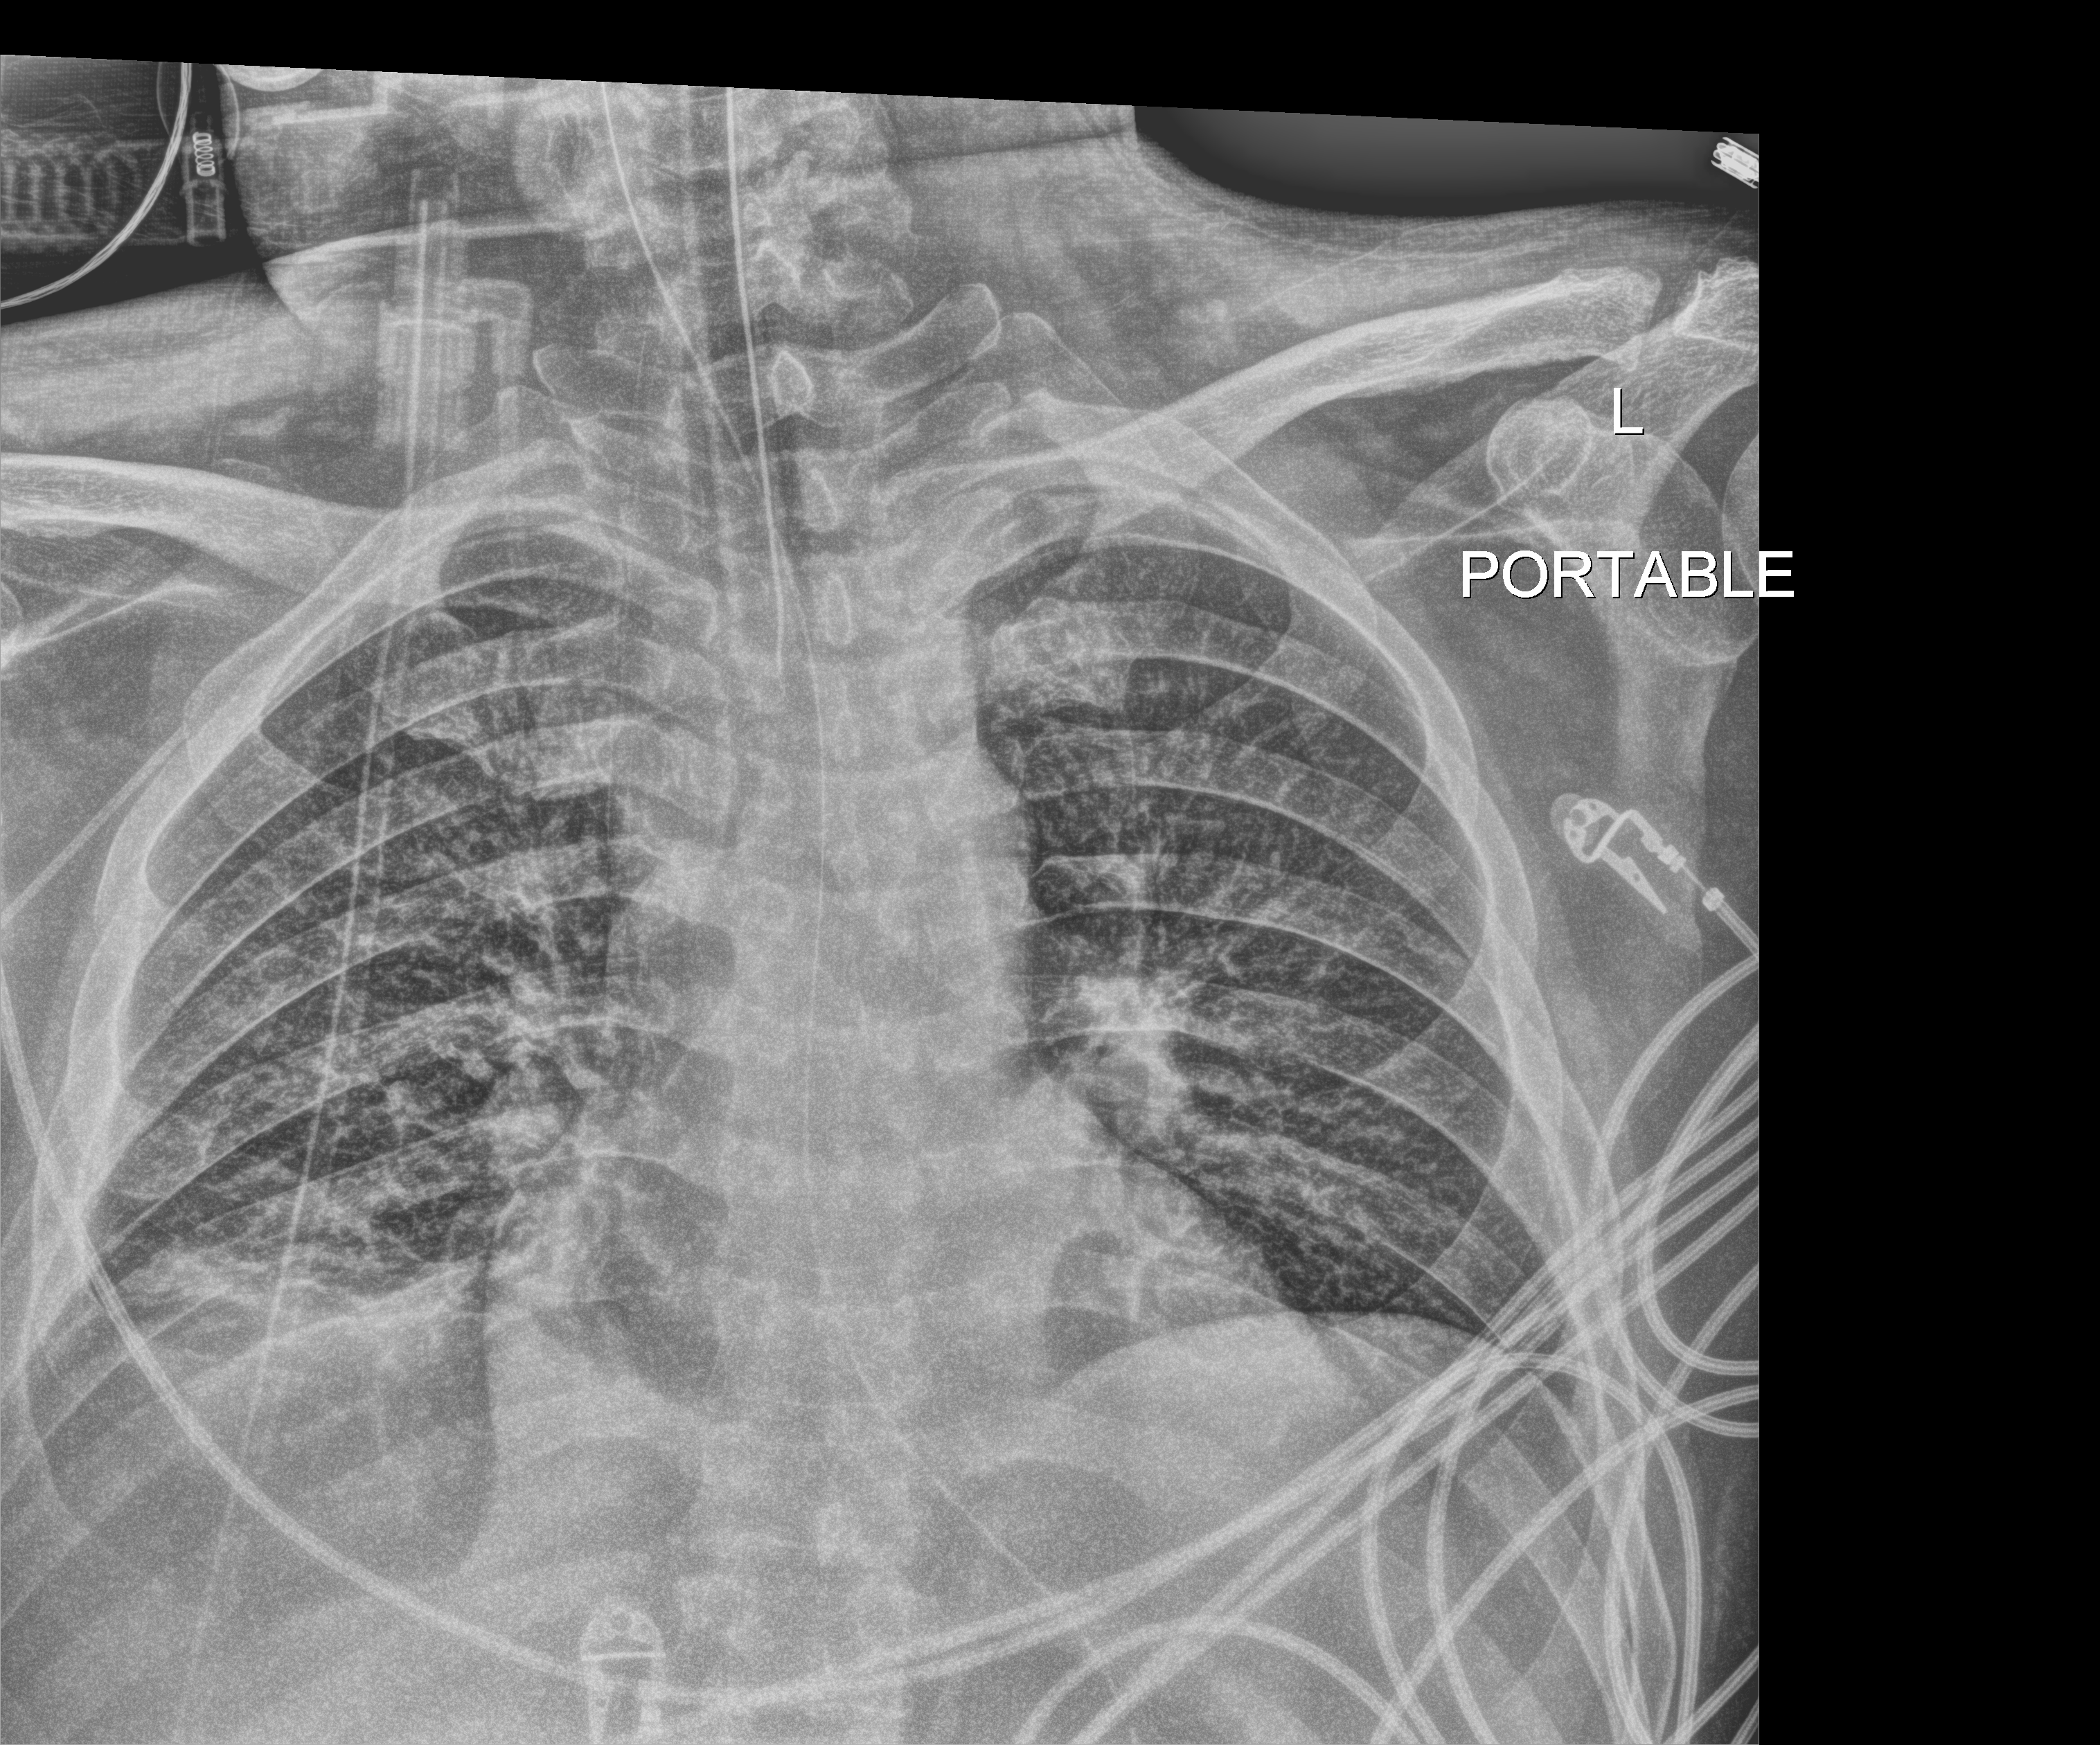
Chest X-ray (portable), anteroposterior (AP) projection. Patient hospitalised with COVID-19; male, aged 18–59 years.
Admission-level facts for this patient (not findings on this image; timing relative to this image not recorded): admitted to intensive care during this hospital stay: yes.